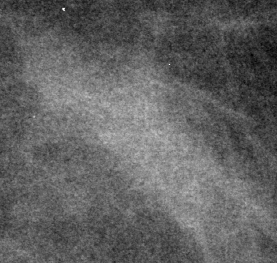
Crop from a digitized film mammogram around one marked abnormality, left breast, CC view, BI-RADS breast density category 1 (scale 1–4).
- Finding: mass, shape irregular, margins ill defined; BI-RADS assessment category 4; pathology (as recorded): benign.